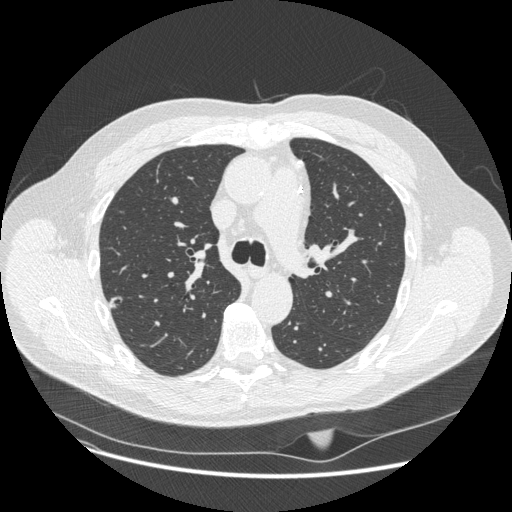
Axial slice from a low-dose chest CT screening exam, second screening round (one year after baseline), lung window (W 1500 / L -600 HU), 1.25 mm slice thickness, slice 75 of 247 in the series, 512 × 512 image matrix, field of view 400 × 400 mm. Male, age 62 years at enrolment.
Lesion marked by an expert reader, bounding box [x1, y1, x2, y2] px = [99, 290, 130, 317]. Screening reader's record for this exam (one nodule recorded; not confirmed to be the boxed lesion): non-calcified nodule or mass ≥4 mm, right upper lobe, 11 × 7 mm, smooth margins, pre-existing on the prior screen: yes. Participant outcome: lung cancer diagnosed 482 days after this screen — adenocarcinoma, NOS, right upper lobe, moderately differentiated (G2), stage IA (AJCC 6th edition), 12 mm at pathology.